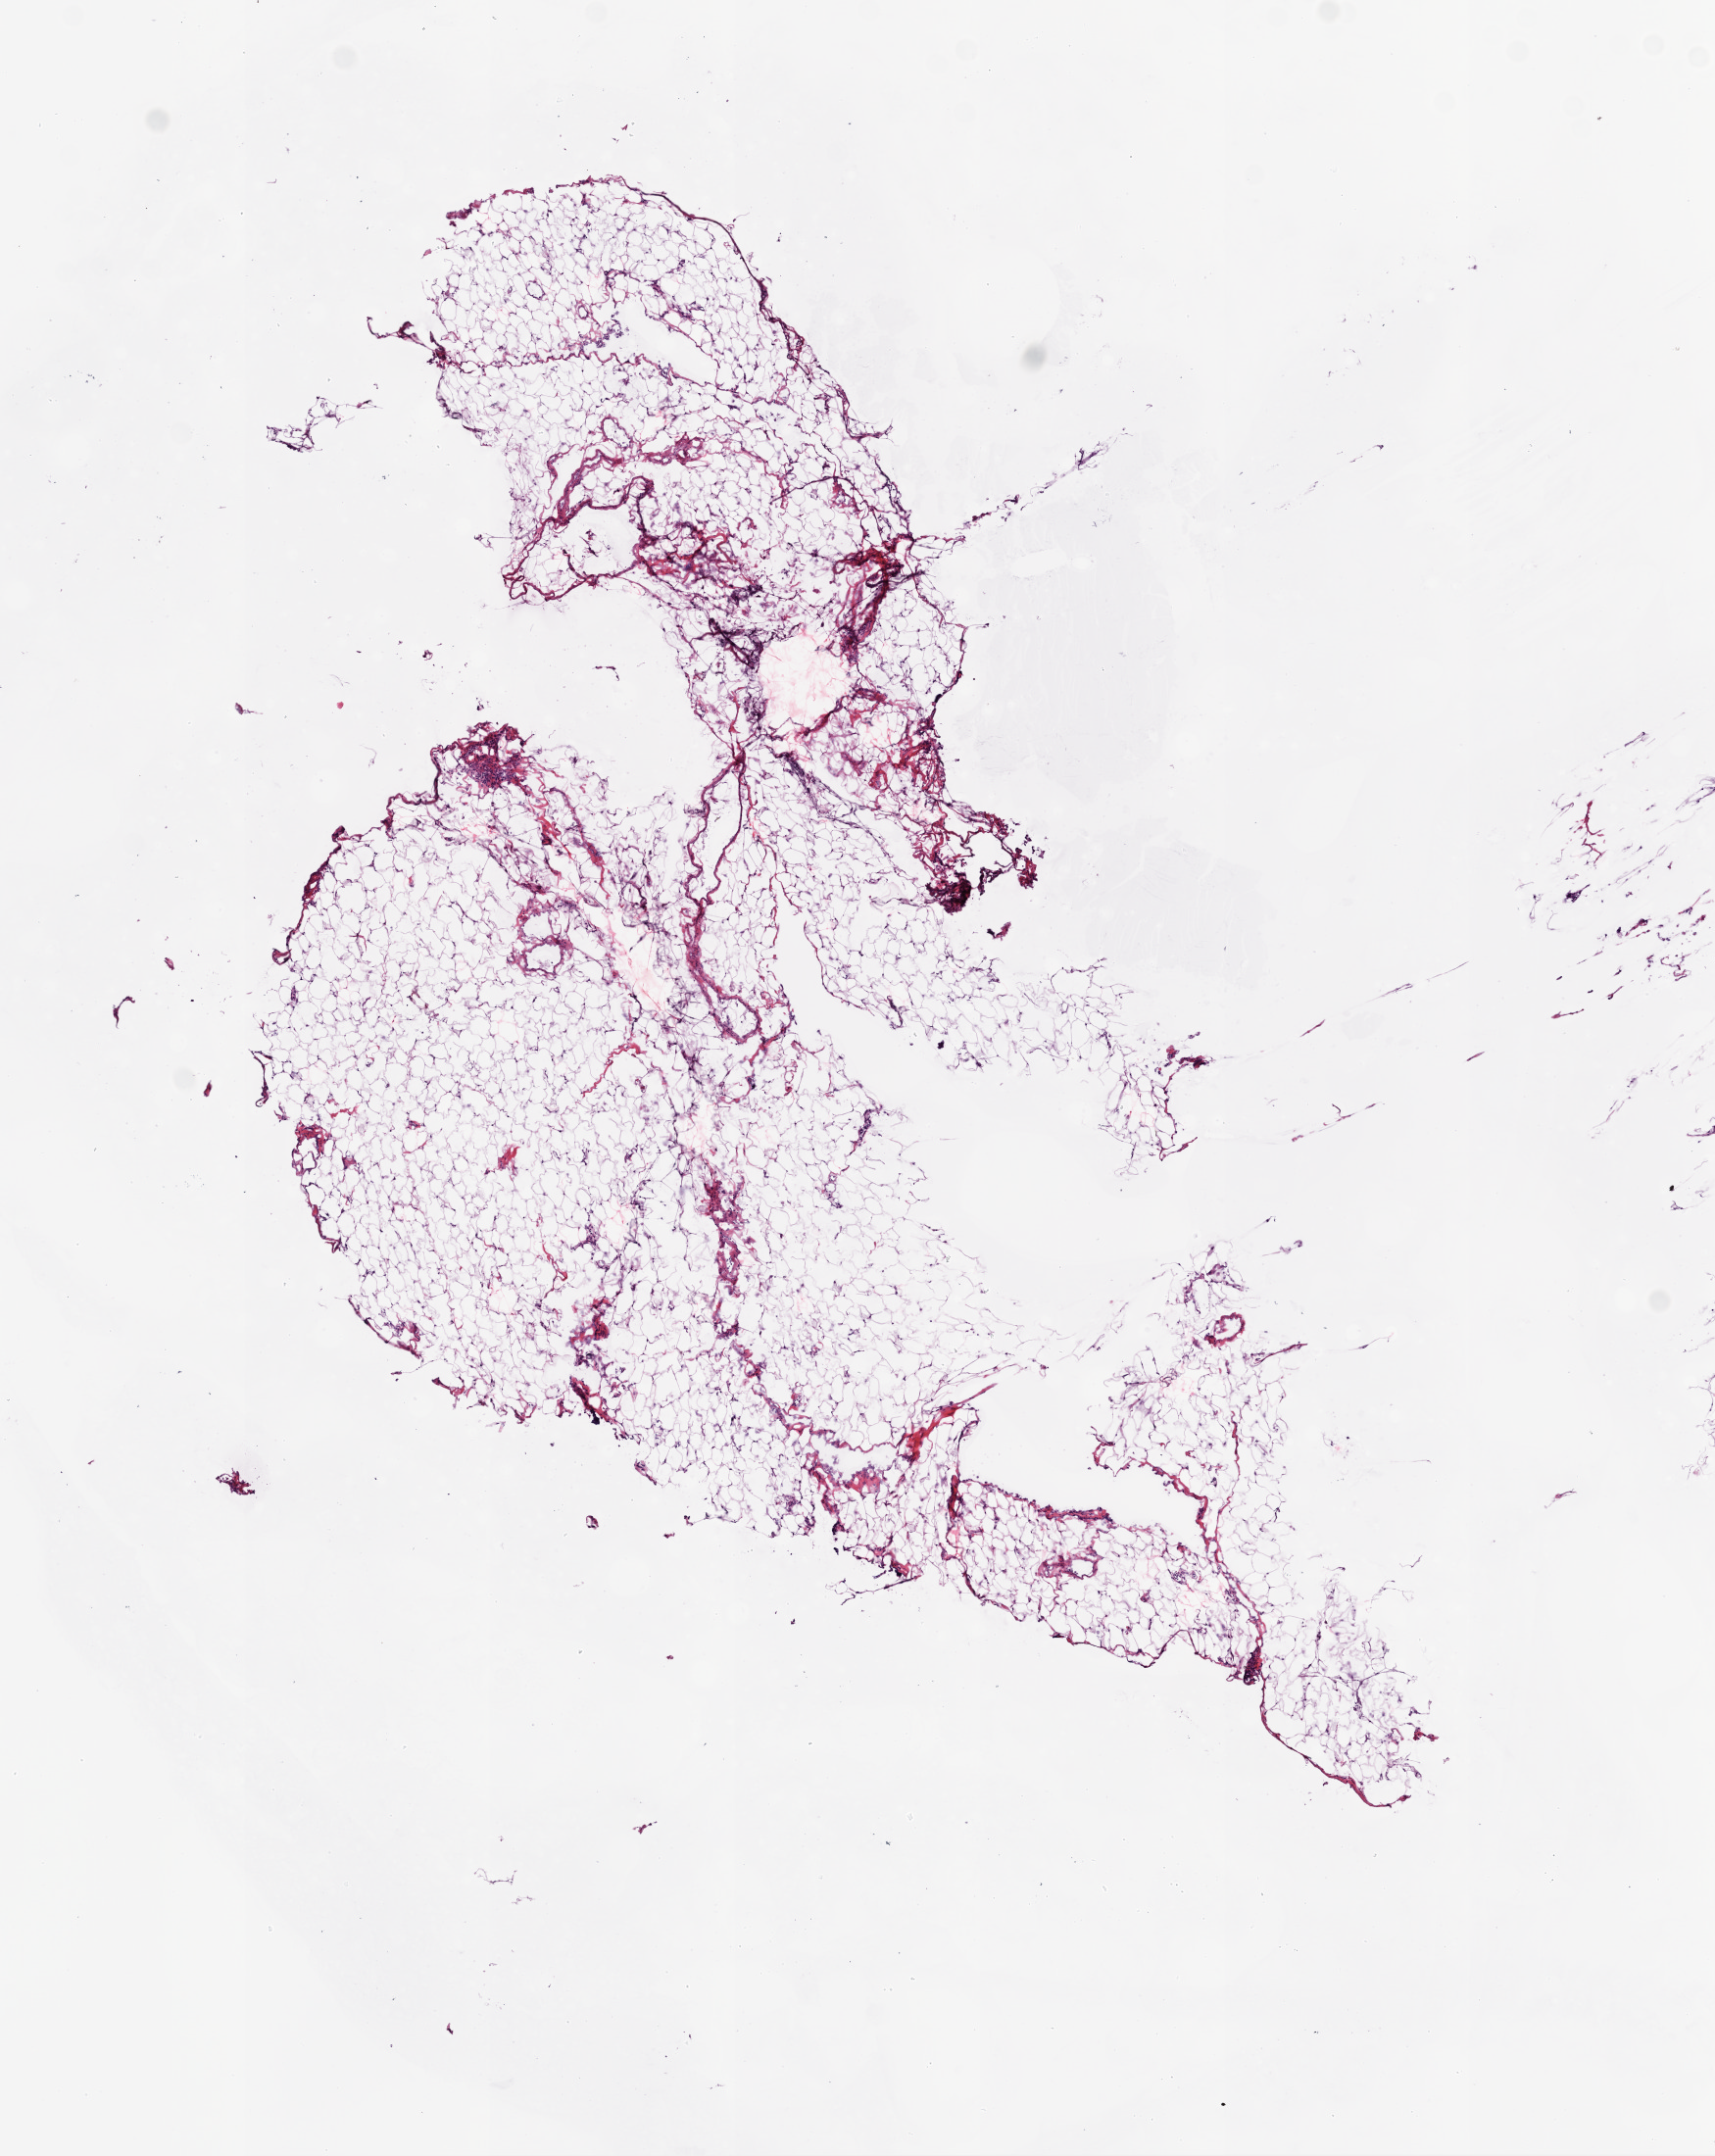
Digitized H&E-stained tissue section (whole slide), whole scanned area (about 7.0 x 8.8 mm, acquisition: 20x scan) shown as a low-resolution overview, frozen section from the bottom of the tissue portion, sample: solid tissue normal (non-tumour tissue), ovary. Female patient; age at initial diagnosis 57 years.
This section: solid tissue normal (non-tumour) sample from the same patient. Patient diagnosis: Serous cystadenocarcinoma, NOS.